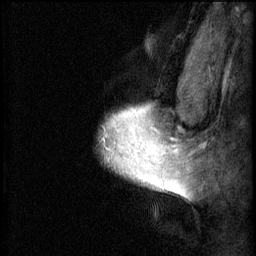
Breast MRI (dynamic contrast-enhanced), one sagittal slice; position 54 of 60 along the scan axis; 3 images stored at this slice position (order not interpretable as contrast timing); 1.5 T; TE 4.2 ms, TR 8.2 ms; 2 mm slice thickness; 256 × 256 image matrix, field of view 180 × 180 mm. Patient: female, 40 years.
Annotated regions visible in this slice (semi-automatically segmented with operator editing):
- analysis volume of interest (the breast-tissue region the enhancement analysis was run in; not a lesion): box from (x=103, y=104) to (x=167, y=193) px
- tumour enhancement mask (voxels above the 70 % enhancement threshold inside the analysis volume of interest): (x=104, y=106)–(x=167, y=191)